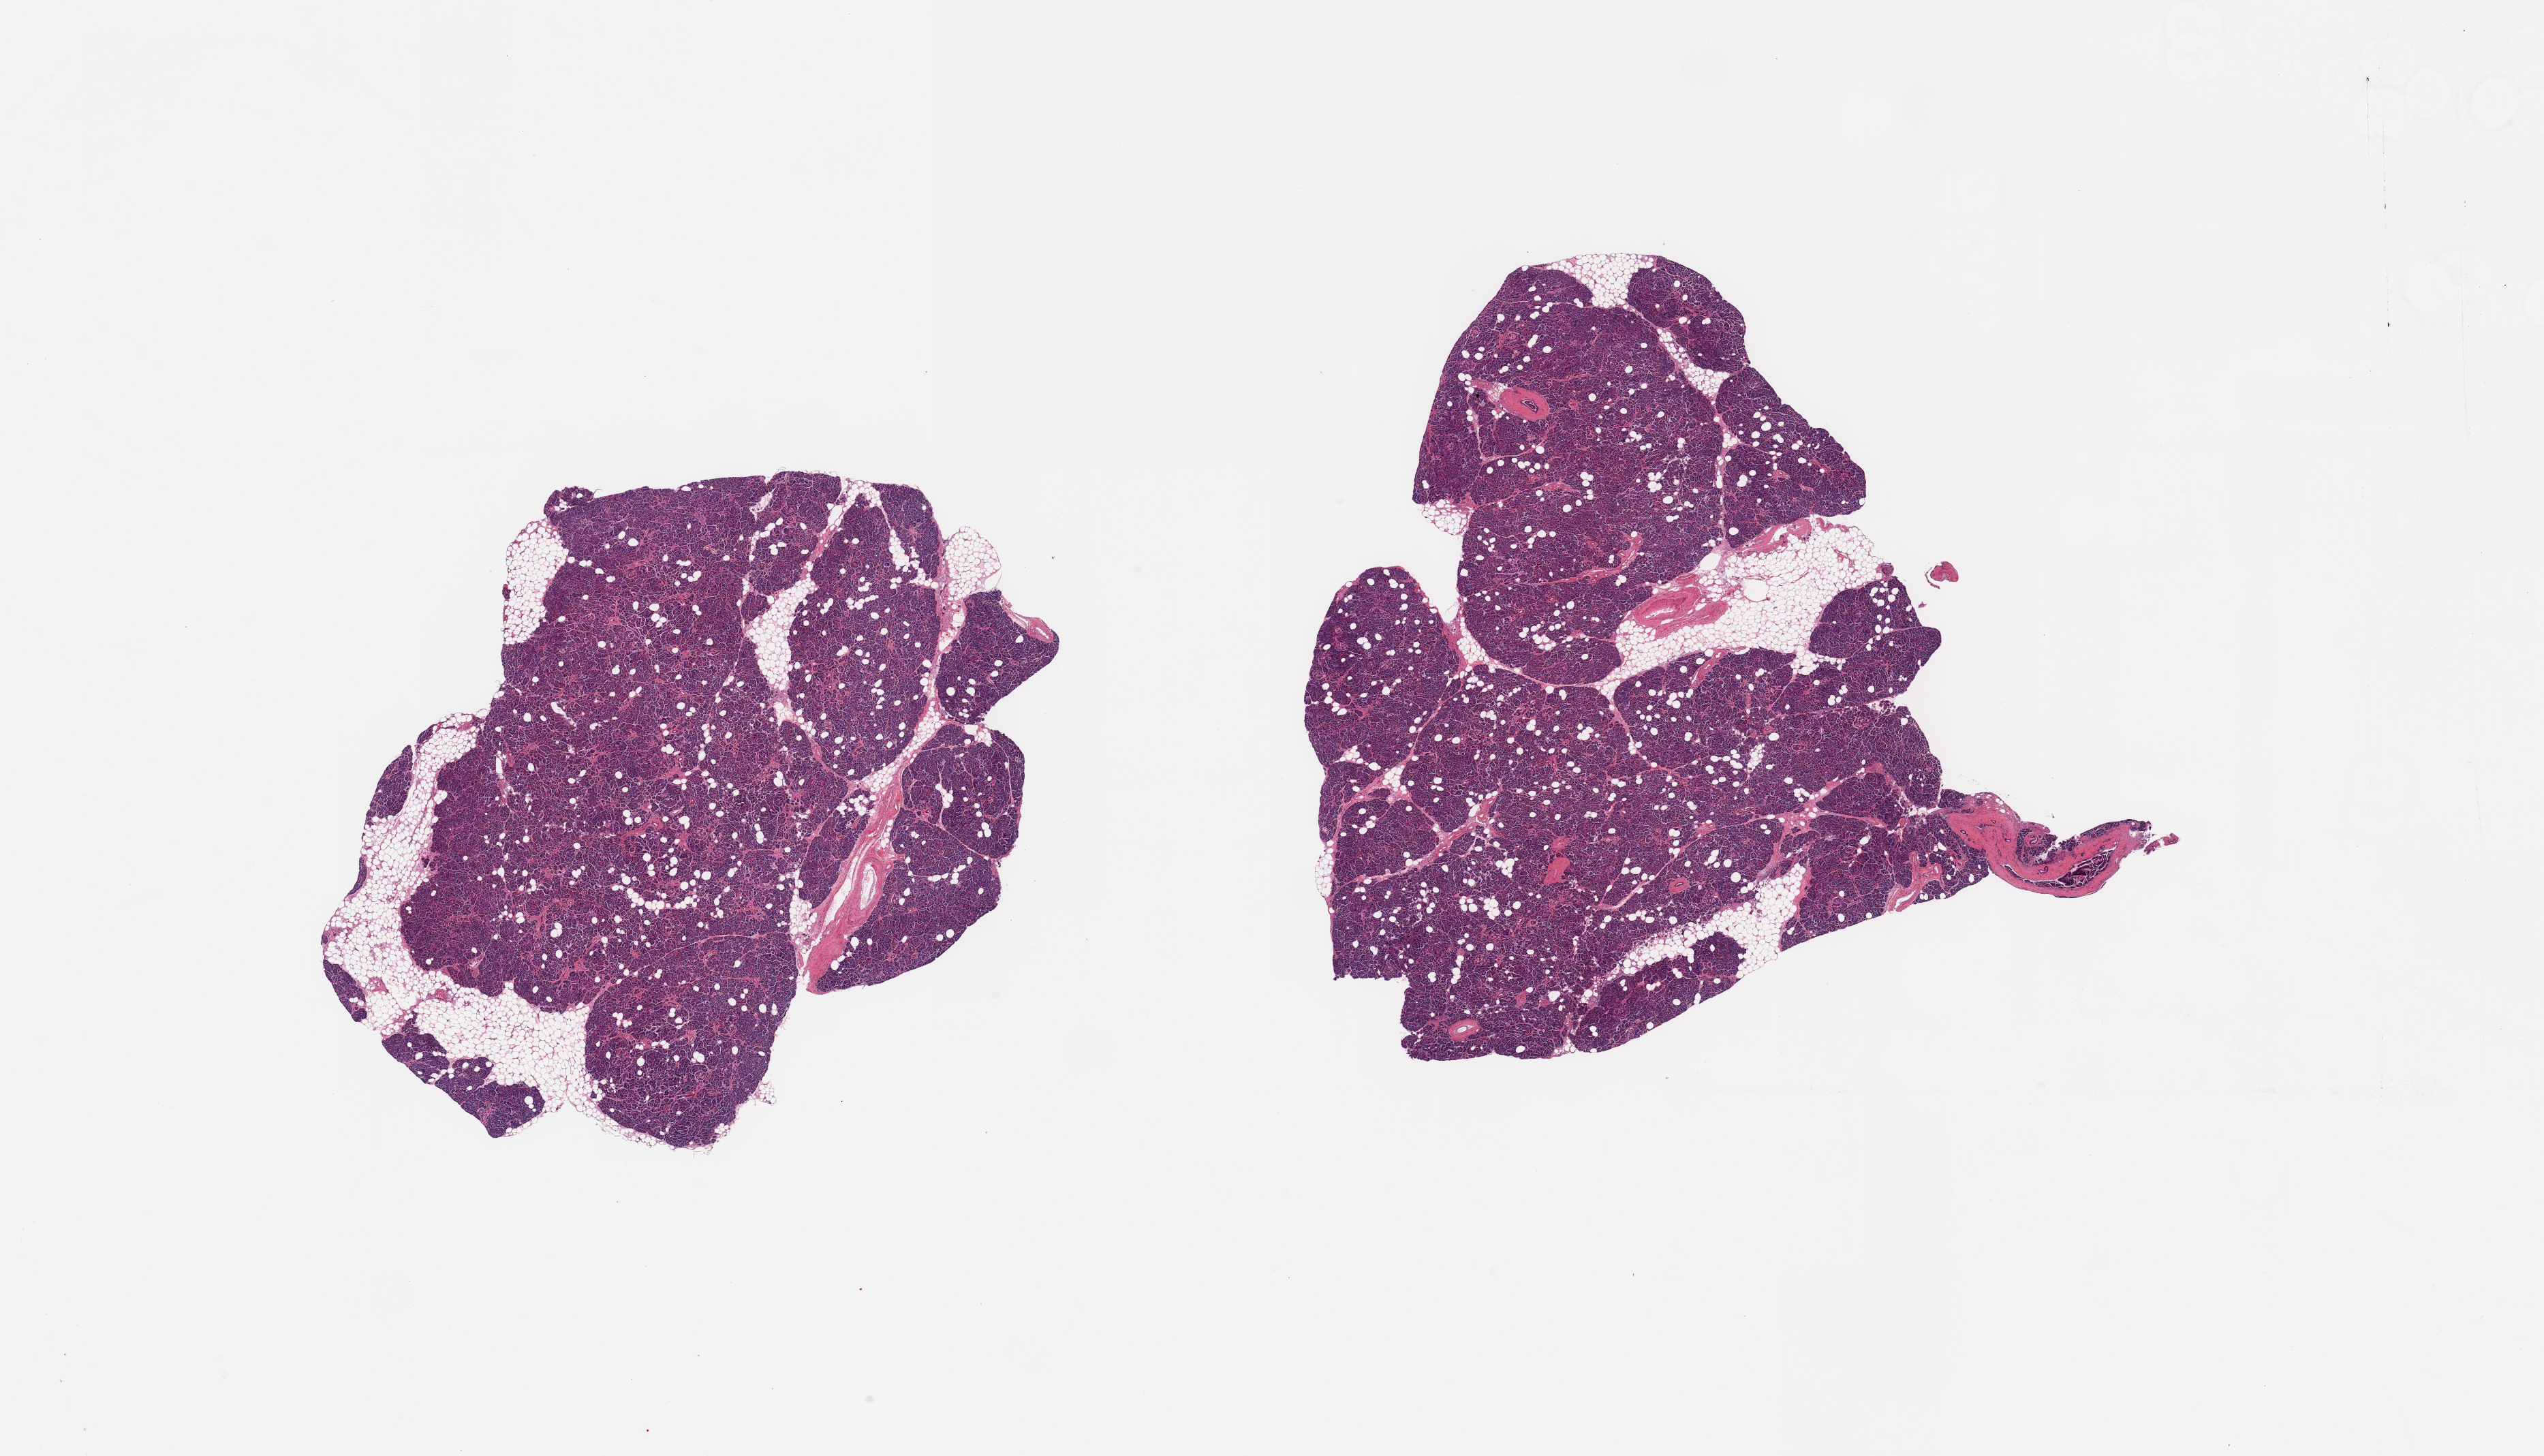
Whole-slide image, H&E stain, brightfield — a low-resolution overview of the entire scanned area, about 29.5 x 16.9 mm (acquisition: 20x scan). PAXgene-fixed paraffin-embedded (PFPE) section. Sampled site (target tissue): pancreas. Donor tissue sample. Donor sex: male.
Pathologist's review note for this sample: 2 pieces; 10% internal fat.